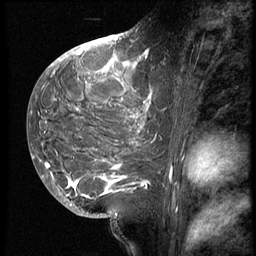
Breast MRI (dynamic contrast-enhanced), one sagittal slice; slice 26 of 62 in the series (ordered by position); 3 images stored at this slice position (order not interpretable as contrast timing); 1.5 T; TE 4.2 ms, TR 9 ms; 256 × 256 image matrix, field of view 180 × 180 mm. Female patient, age 28 years. Case-level facts recorded for this patient, not image findings: setting: breast cancer imaged before/during neoadjuvant chemotherapy.
Outlined on this slice (semi-automatic segmentation, software-assisted and operator-edited):
- analysis volume of interest (the breast-tissue region the enhancement analysis was run in; not a lesion): bounding box (x1, y1, x2, y2) in pixels: (42, 45, 164, 207)
- tumour enhancement mask (voxels above the 140 % enhancement threshold inside the analysis volume of interest): (45, 49, 152, 198)